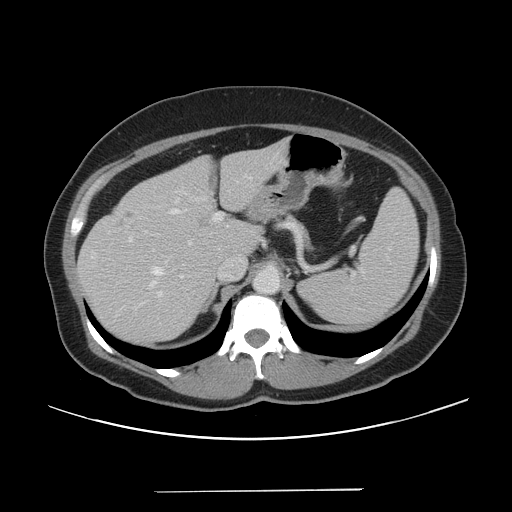
Contrast-enhanced abdominal CT, one axial slice. Slice 30 of 56 in the series (ordered by position). Intravenous contrast given. Soft-tissue window (W 400 / L 40 HU). 5 mm slice thickness. 512 × 512 image matrix. Female patient, age 54 years. Case-level facts recorded for this patient, not image findings: diagnosis: colorectal cancer liver metastases, imaged before liver resection; multiple liver metastases: yes.
Outlined on this slice (manually delineated by an expert):
- hepatic veins: box from (x=153, y=192) to (x=190, y=275) px
- liver: (x=78, y=138)–(x=291, y=345)
- planned liver remnant (the part of the liver to remain after resection): (x=180, y=138)–(x=291, y=257)
- portal vein (with intrahepatic branches): (x=158, y=178)–(x=242, y=296)
- liver metastasis: (x=119, y=212)–(x=136, y=226)